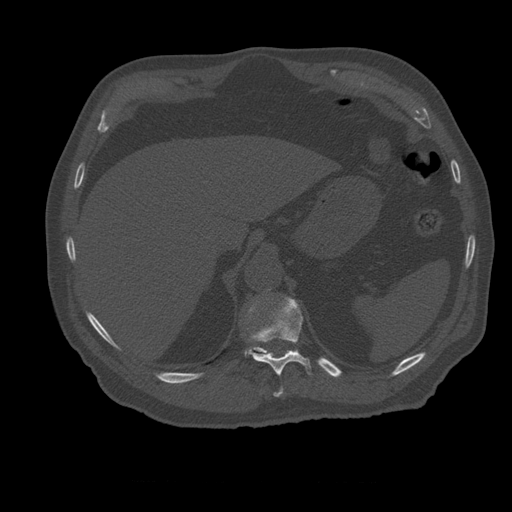
CT including the spine, one axial slice; position 279 of 399 along the scan axis; 120 kVp; bone window (W 1800 / L 400 HU); 1.25 mm slice thickness; 512 × 512 image matrix, field of view 407 × 407 mm. Patient age 73 years. Case-level facts recorded for this patient, not image findings: primary cancer: prostate; vertebrae with lytic lesions (as recorded): L2.
Outlined on this slice (semi-automatic segmentation, software-assisted and operator-edited):
- T10 vertebra: bounding box <274,388,283,398> (left, top, right, bottom; pixels)
- T11 vertebra: <250,298,312,376>
- T12 vertebra: <245,301,291,357>